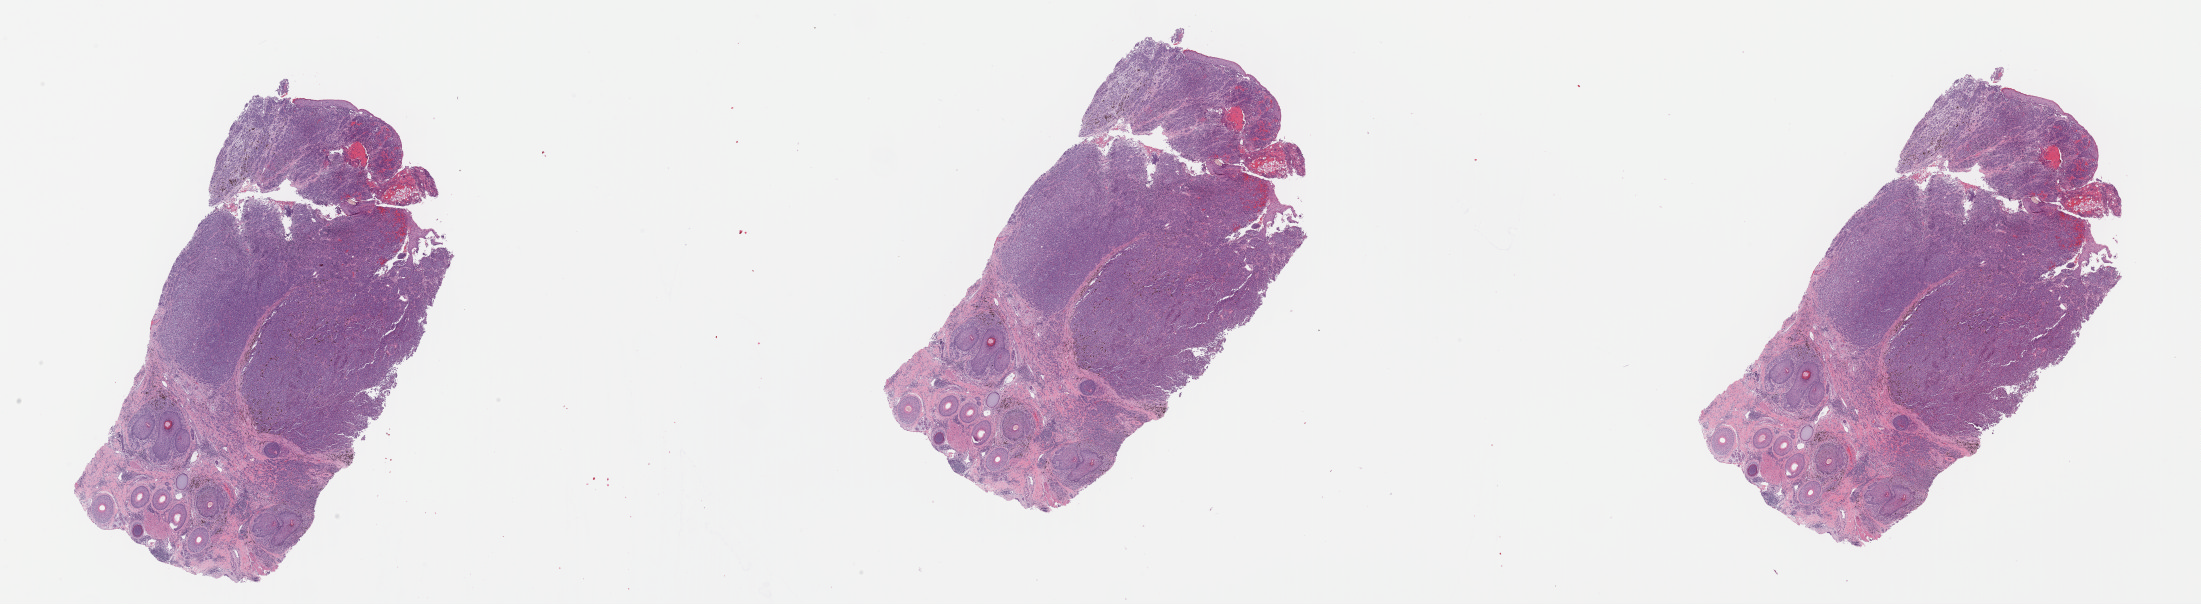
Whole-slide histology image, H&E-stained, a low-resolution overview of the entire scanned area, about 34.8 x 9.5 mm; formalin-fixed paraffin-embedded (FFPE) diagnostic section; primary tumour sample from the skin. Male patient; age at initial diagnosis 48 years.
- histologic diagnosis: Malignant melanoma, NOS